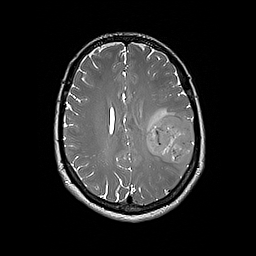
Brain MRI from a brain-tumour surgery series, one axial slice. Slice 80 of 192 in the series (ordered by position). 1 mm slice thickness. 256 × 256 image matrix, field of view 250 × 250 mm. From the clinical record (not read from this slice): histopathology: Glioblastoma; WHO grade: 4; IDH mutation: no; tumour location: Left Frontal.
Outlined on this slice (outlined manually by an expert reader):
- tumour: bounding box (x1, y1, x2, y2) in pixels: (147, 115, 195, 165)